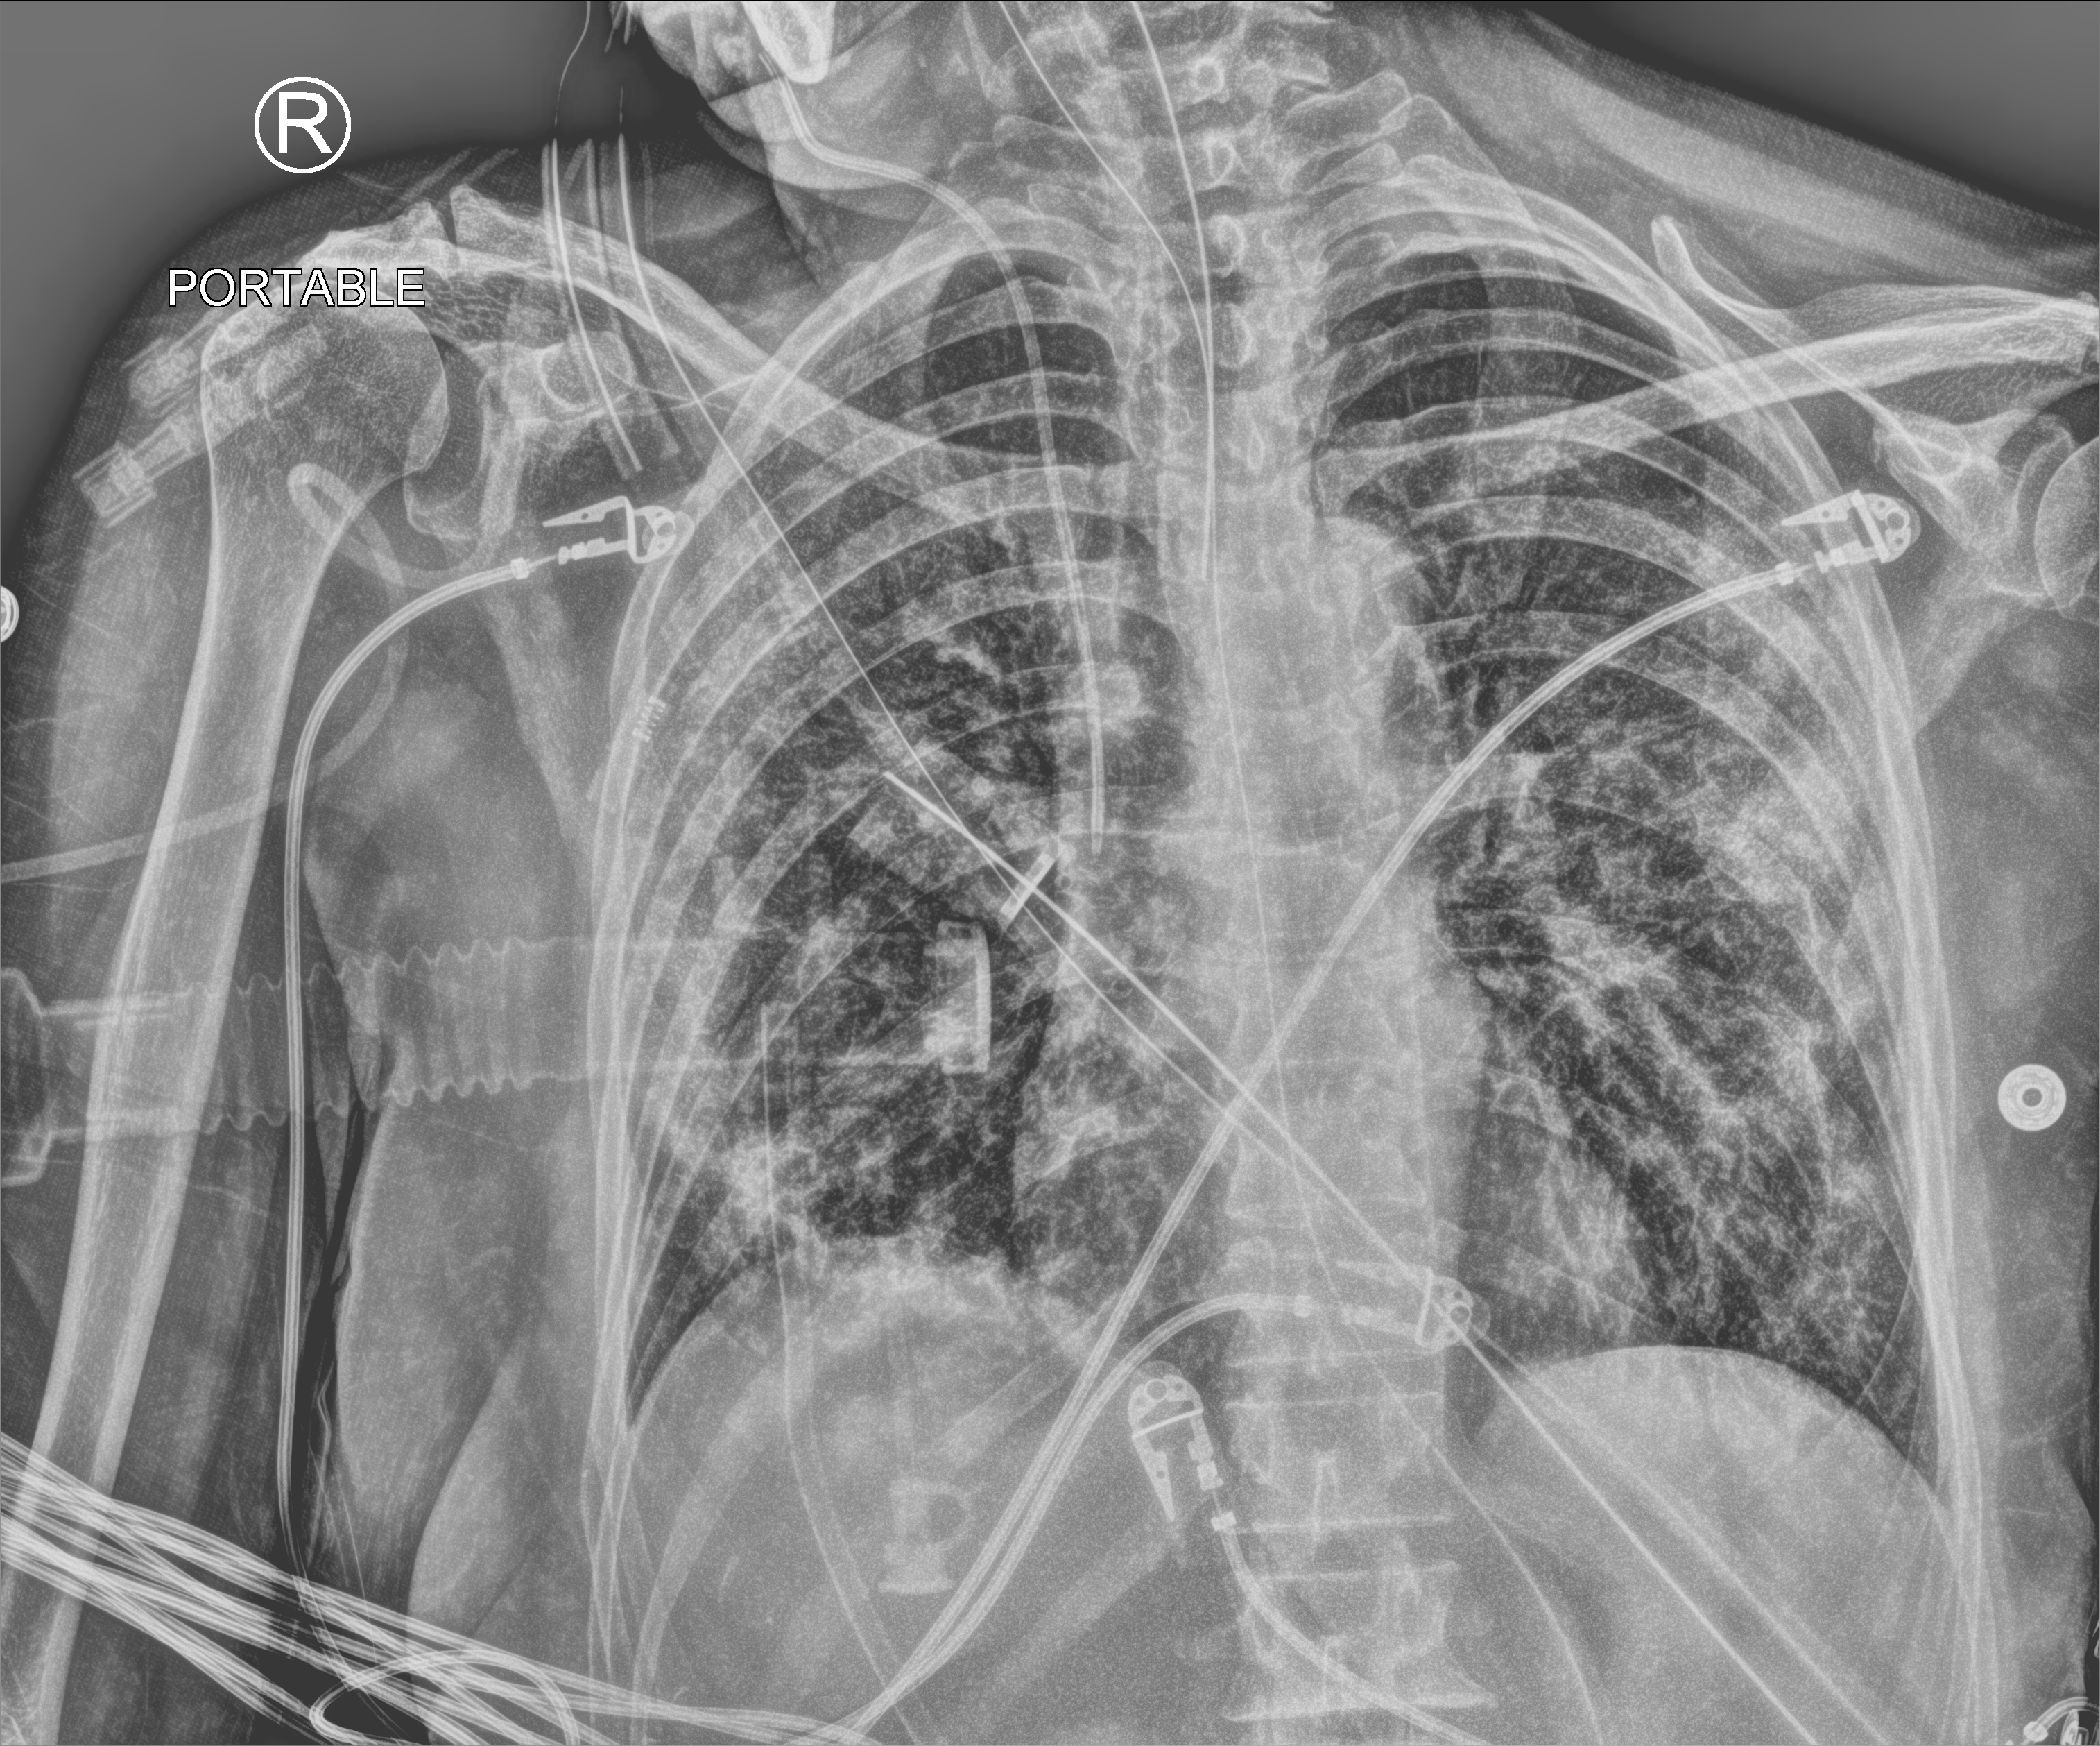
Bedside chest radiograph (computed radiography), anteroposterior (AP) projection. Patient hospitalised with COVID-19; female, aged 60–74 years.
From the hospital-stay record, not from the radiograph (when in the stay this image was taken is not recorded): other chronic lung disease (admission record): no; mechanically ventilated during this hospital stay: yes; admitted to intensive care during this hospital stay: yes.